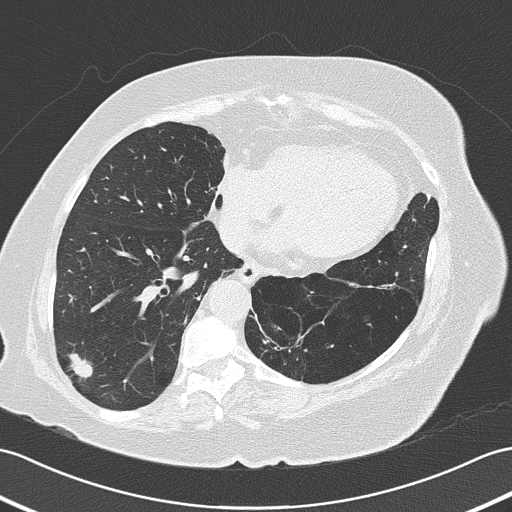
Low-dose screening chest CT, axial slice, baseline screening round, lung window (W 1500 / L -600 HU), 2 mm slice thickness, slice 100 of 161 in the series. Female, age 73 years at enrolment. Former smoker at enrolment.
- Lesion marked by an expert reader, bounding box <54,338,101,386> (left, top, right, bottom; pixels).
- The screening reader recorded 4 non-calcified nodules or masses ≥4 mm on this exam; which of them this box marks is not recorded.
- Official screen result: positive, change unspecified: nodule(s) >= 4 mm or enlarging nodule(s), mass(es), or other non-specific abnormalities suspicious for lung cancer.
- Later outcome: lung cancer diagnosed 50 days after this screen — adenocarcinoma, NOS, right lower lobe, poorly differentiated (G3), stage IB (AJCC 6th edition), 17 mm at pathology.